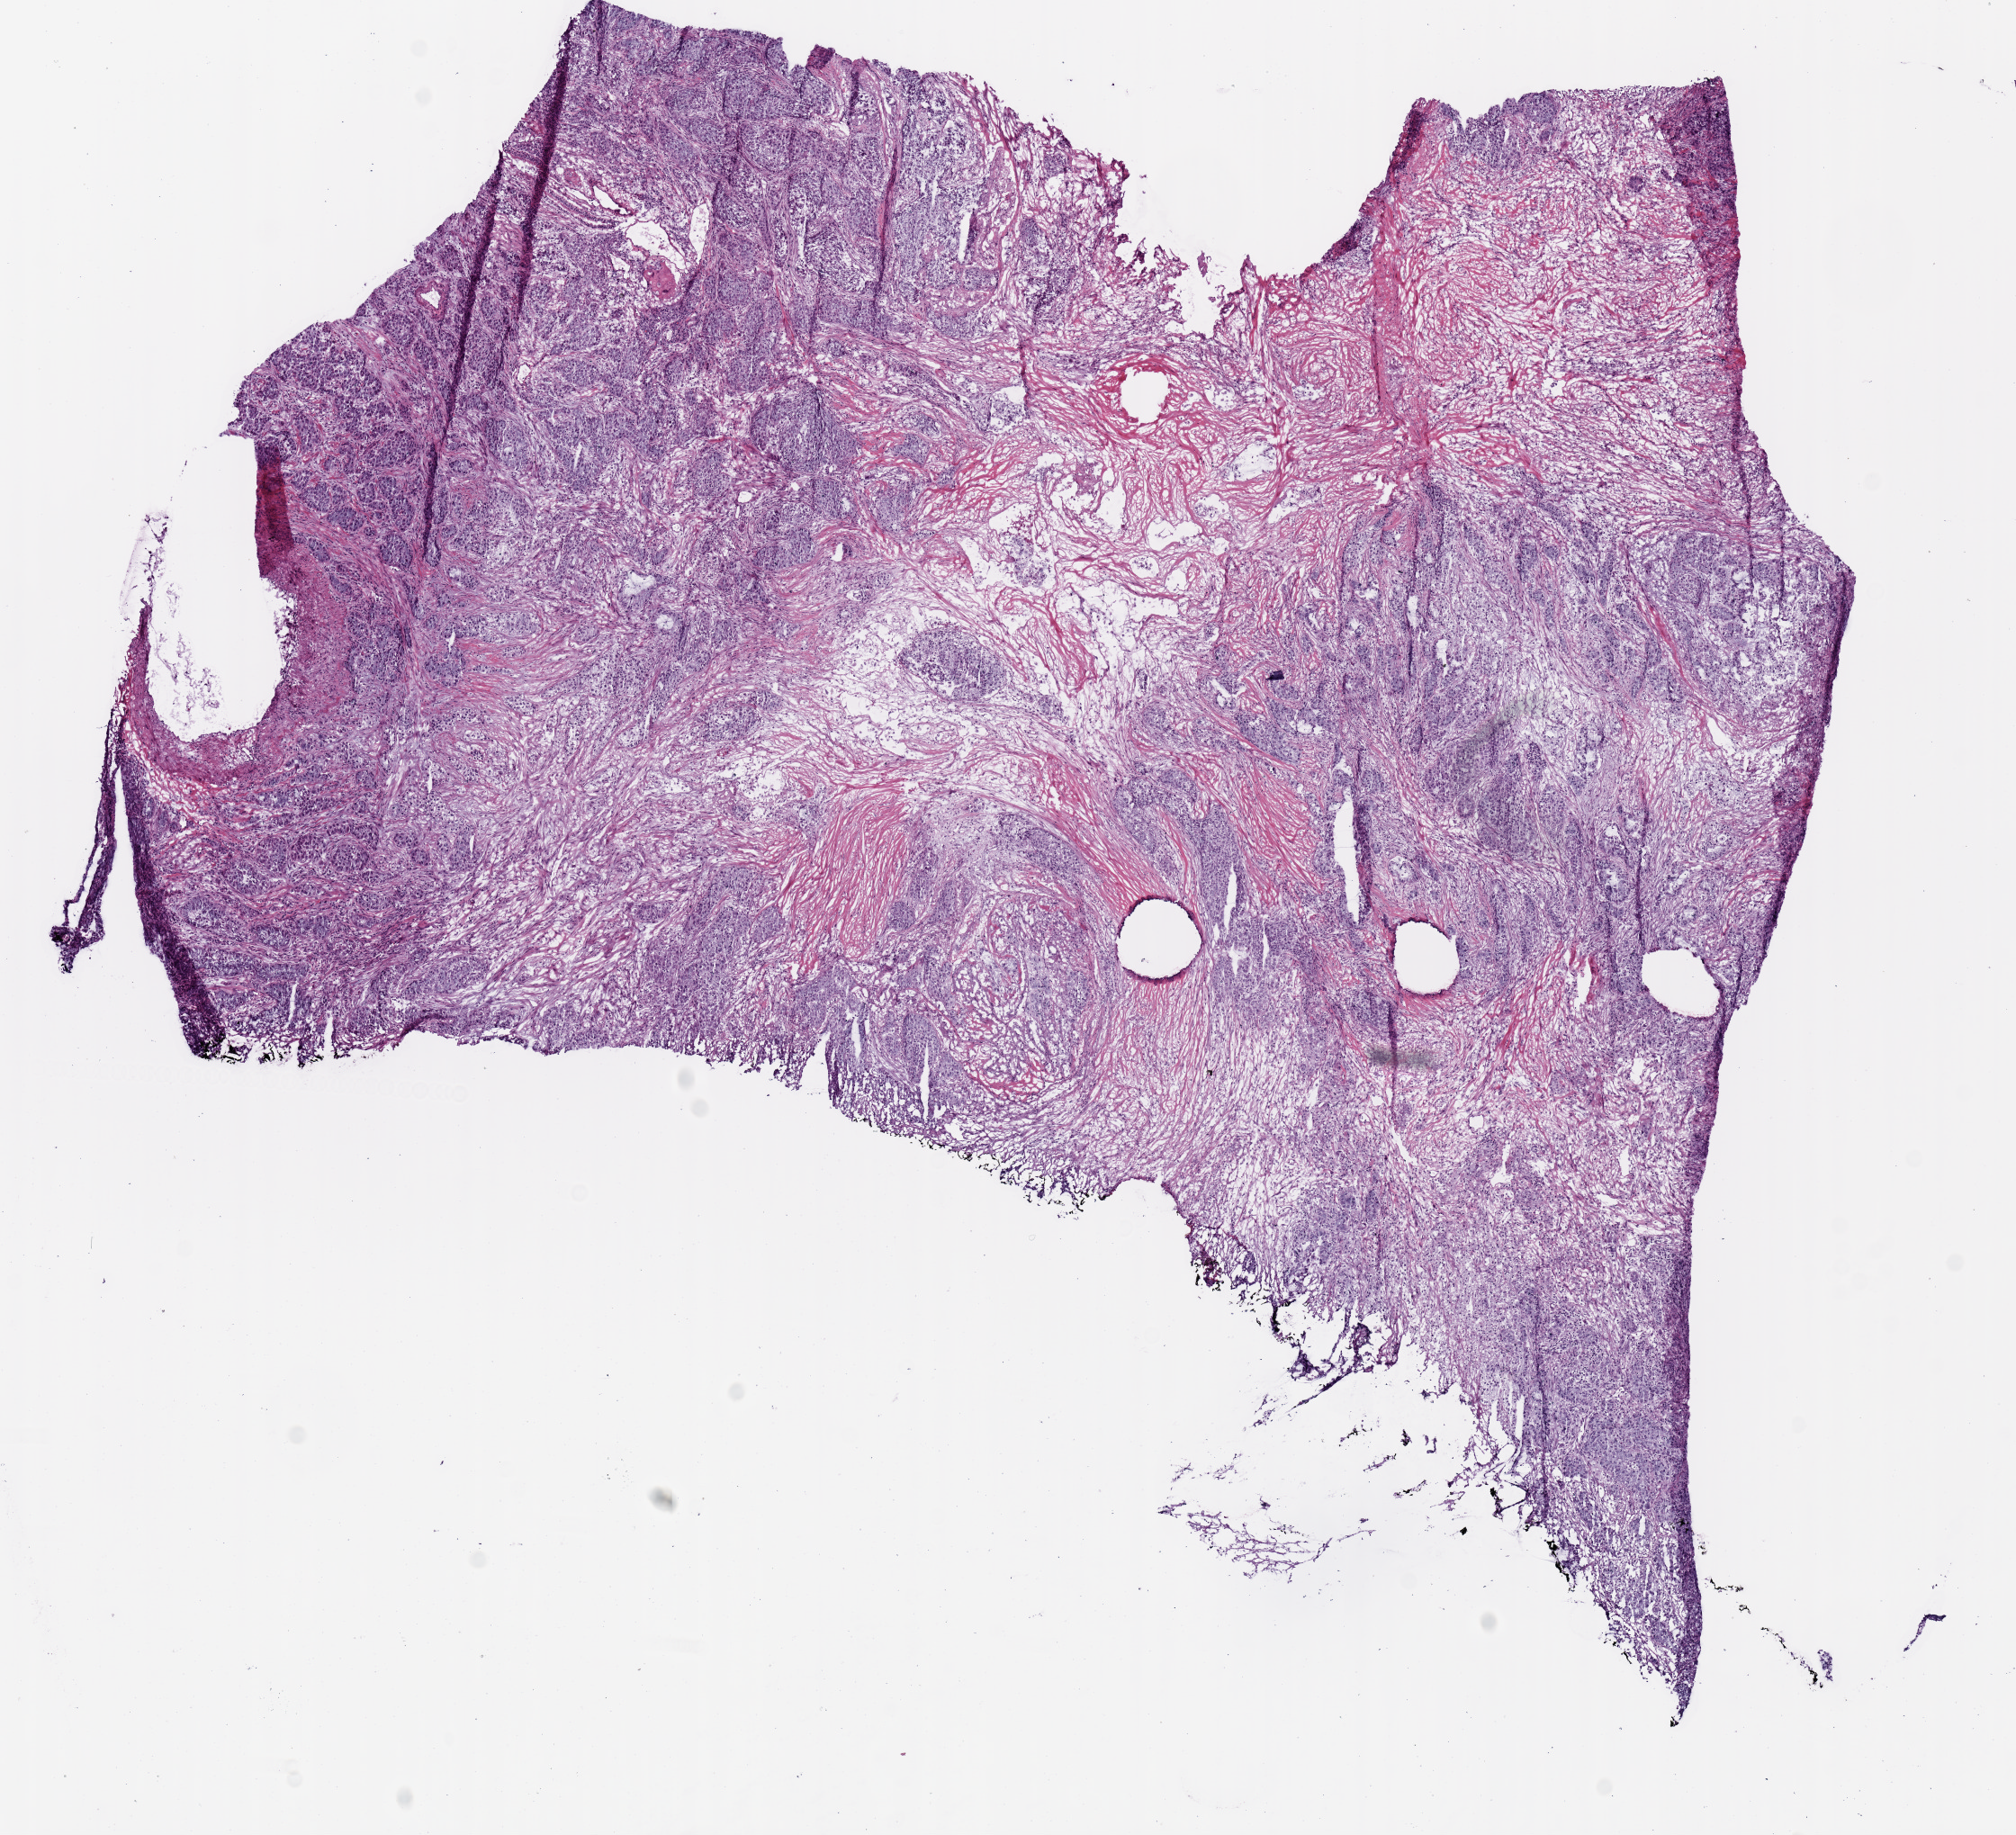
Digitized H&E tissue section (whole slide), shown as a low-resolution overview of the whole scanned area (about 8.9 x 8.1 mm, from a 20x scan). Frozen section from the top of the tissue portion. Sample: primary tumour, lung. Male, age 74 years at initial diagnosis. Composition of this section per pathologist review: tumour cells 68%, tumour nuclei 75%.
Pathologic diagnosis: Adenocarcinoma, NOS (lower lobe, lung).